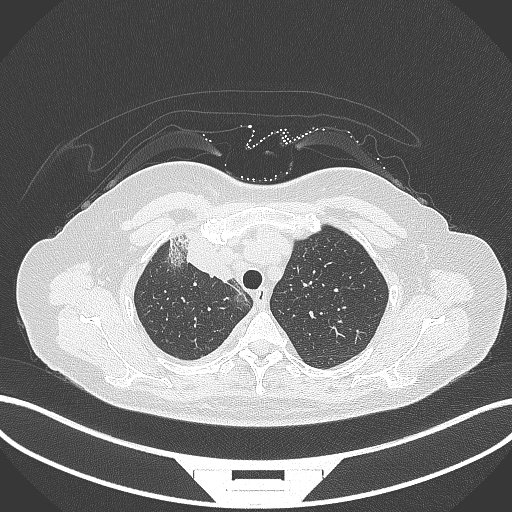
Chest CT, one axial slice. Slice 247 of 305 in the series (ordered by position). Reconstruction kernel B70f. Lung window (W 1500 / L -600 HU). 1 mm slice thickness. 512 × 512 image matrix, field of view 400 × 400 mm. Patient: female, 52 years. From the clinical record (not read from this slice): clinical TNM (as recorded): T3 N1 M1.
Annotated regions visible in this slice (bounding box drawn by a radiologist):
- lung tumour (recorded histology: adenocarcinoma): box from (x=167, y=233) to (x=237, y=280) px